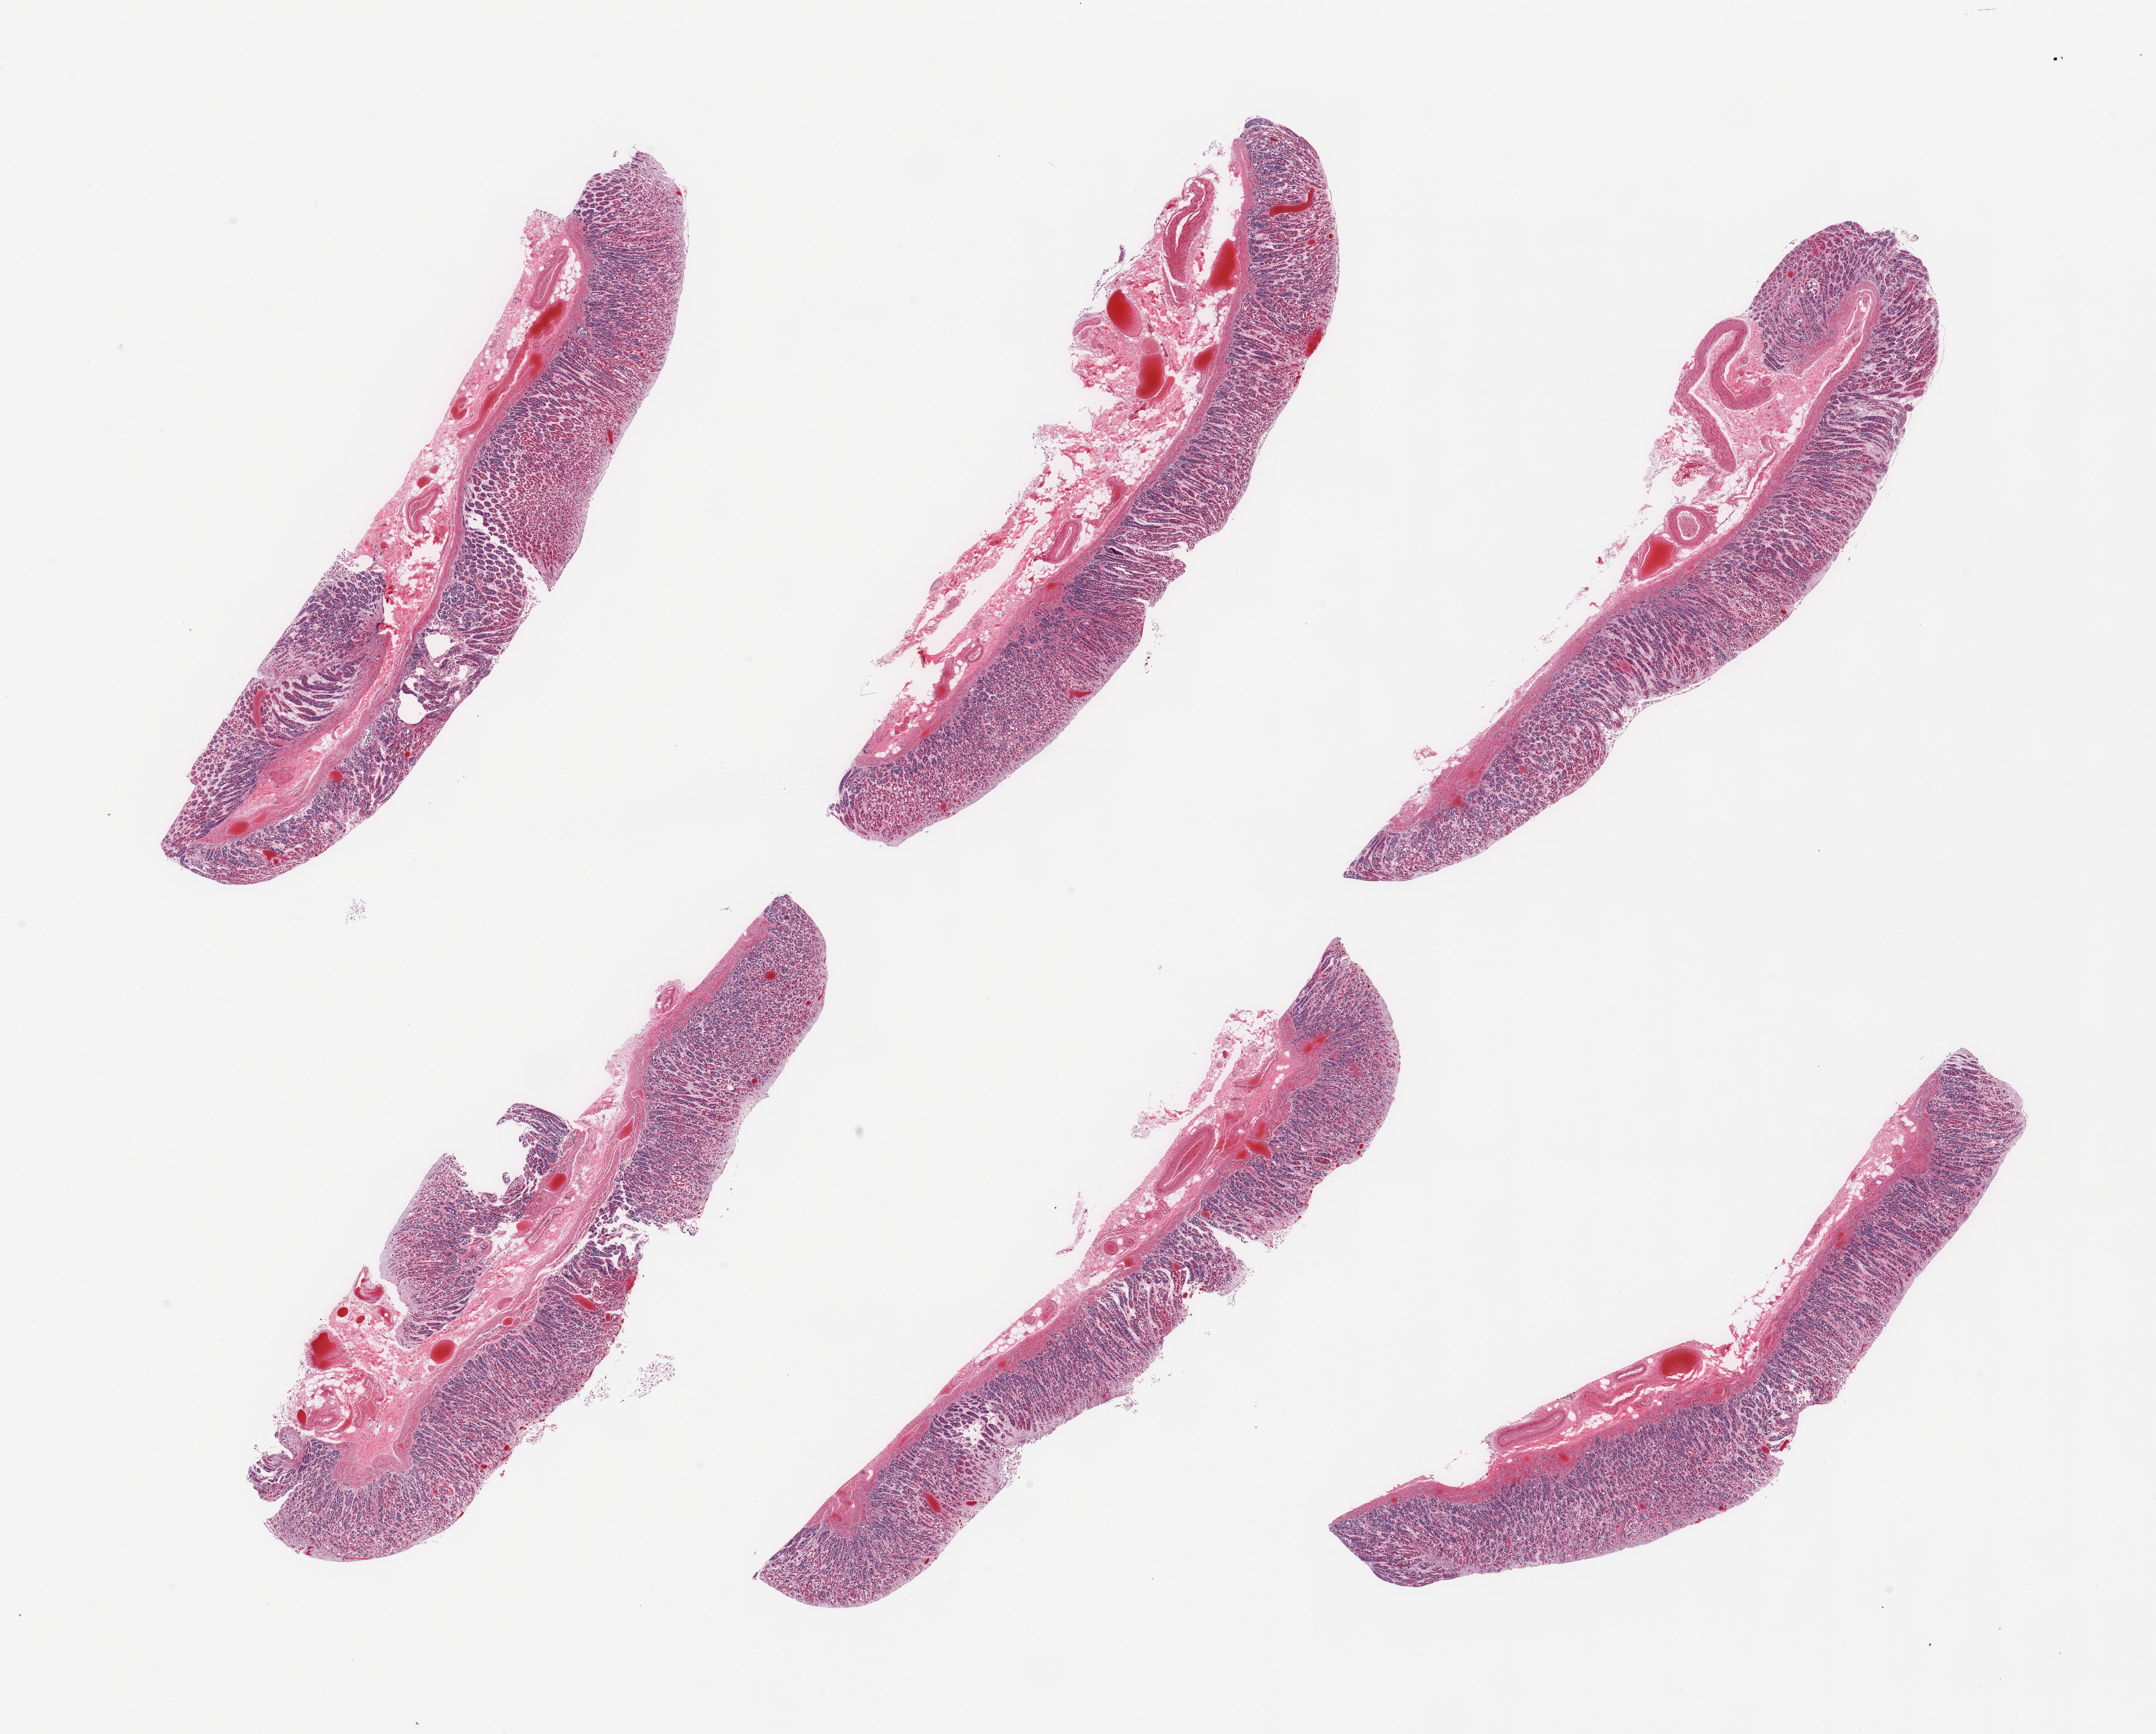
Digitized hematoxylin and eosin (H&E)-stained section, low-resolution overview of the scanned area, about 26.6 x 21.4 mm (from a 20x scan); PAXgene-fixed, paraffin-embedded tissue; target tissue: stomach; donor tissue sample. Donor sex: male.
* pathologist's review note for this sample: 6 pieces